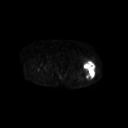
FDG PET of an extremity soft-tissue mass (from a PET/CT study), one axial slice; 3.27 mm slice thickness; 128 × 128 image matrix. Patient: female, 62 years. Case-level facts recorded for this patient, not image findings: histological type: undifferentiated – high grade; grade: high; site of the primary tumour: left thigh.
Annotated regions visible in this slice (expert contour drawn on MRI and transferred to this co-registered scan by the dataset authors):
- gross tumour volume including surrounding oedema: bounding box (x1, y1, x2, y2) in pixels: (83, 61, 95, 80)
- gross tumour volume (mass): (83, 61, 95, 80)